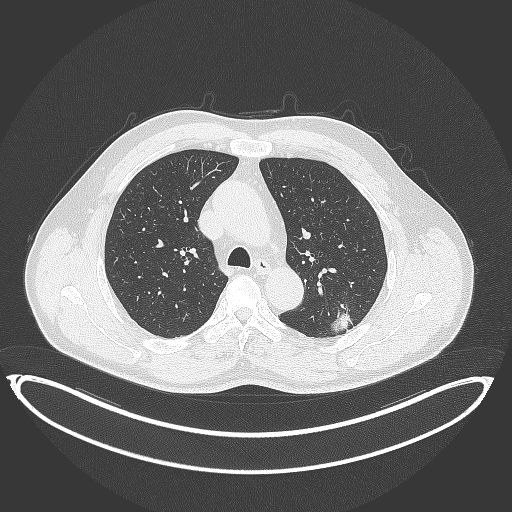
Chest CT, one axial slice. Position 250 of 399 along the scan axis. Lung window (W 1500 / L -600 HU). 1 mm slice thickness. 512 × 512 image matrix, field of view 469 × 469 mm. Patient: male, 58 years. From the clinical record (not read from this slice): clinical TNM (as recorded): T1c N0 M0; histopathological grade: G1-2.
Structures marked on this image (rectangle marked by the reading radiologist):
- lung tumour (recorded histology: adenocarcinoma): bounding box (x1, y1, x2, y2) in pixels: (332, 300, 361, 339)